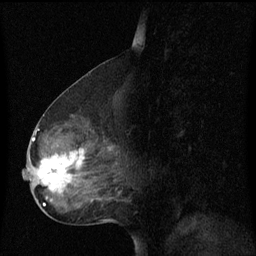
Breast MRI (dynamic contrast-enhanced), one sagittal slice; slice 35 of 60 in the series (ordered by position); dynamic contrast-enhanced series, image 2 of 3 at this slice position (ordered by acquisition); 1.5 T; TE 4.2 ms, TR 8.4 ms; 256 × 256 image matrix. Patient: female, 49 years. From the clinical record (not read from this slice): setting: breast cancer imaged before/during neoadjuvant chemotherapy; receptor status: HR-positive, HER2-negative.
Outlined on this slice (semi-automatic segmentation, software-assisted and operator-edited):
- analysis volume of interest (the breast-tissue region the enhancement analysis was run in; not a lesion): bounding box <23,126,121,201> (left, top, right, bottom; pixels)
- tumour enhancement mask (voxels above the 70 % enhancement threshold inside the analysis volume of interest): <33,138,86,193>